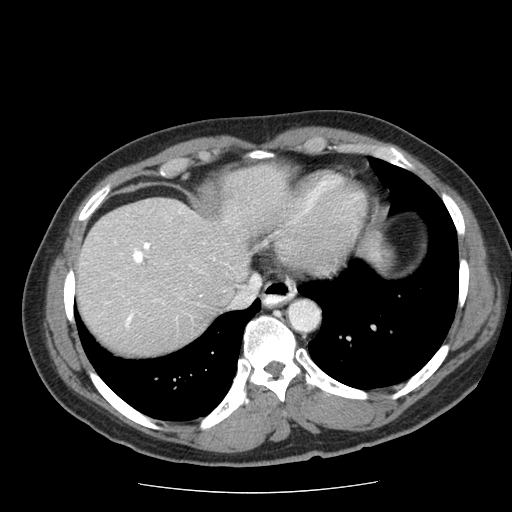
Contrast-enhanced abdominal CT (liver protocol), one axial slice. Slice 58 of 85 in the series (ordered by position). Soft-tissue window (W 400 / L 40 HU). 2.5 mm slice thickness. 512 × 512 image matrix, field of view 360 × 360 mm. From the clinical record (not read from this slice): diagnosis: hepatocellular carcinoma (patient treated with transarterial chemoembolisation; whether this scan precedes or follows treatment is not stated here); TNM stage (as recorded): Stage-IIIA; Child-Pugh class: A; tumour differentiation: well differentiated; tumour size: 8 cm.
Outlined on this slice (semi-automatically segmented with operator editing):
- liver parenchyma outside the tumour (the mass and vessels are separate outlines, so this box may not span the whole liver): bounding box <76,164,284,354> (left, top, right, bottom; pixels)
- liver vessels: <107,211,215,327>